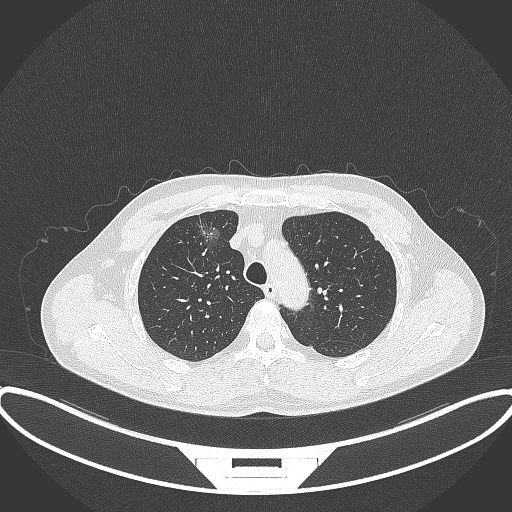
Chest CT, one axial slice; lung window (W 1500 / L -600 HU); 512 × 512 image matrix, field of view 424 × 424 mm. Male patient, age 60 years. From the clinical record (not read from this slice): clinical TNM (as recorded): T1c N0 M0.
Outlined on this slice (rectangle marked by the reading radiologist):
- lung tumour (recorded histology: adenocarcinoma): bounding box [x1, y1, x2, y2] px = [197, 216, 224, 260]